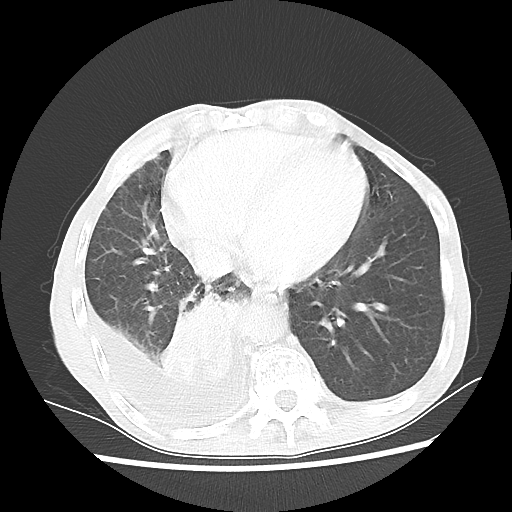
Chest CT, one axial slice. Slice 20 of 60 in the series (ordered by position). Lung window (W 1500 / L -600 HU). 5 mm slice thickness. 512 × 512 image matrix, field of view 335 × 335 mm. Patient: male, 76 years. Case-level facts recorded for this patient, not image findings: clinical TNM (as recorded): T3 N3 M1a.
Structures marked on this image (bounding box drawn by a radiologist):
- lung tumour (recorded histology: squamous cell carcinoma): bounding box [x1, y1, x2, y2] px = [158, 286, 243, 392]